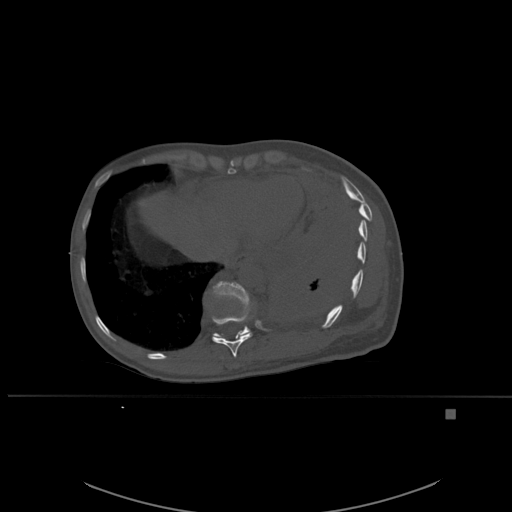
CT including the spine, one axial slice. Slice 312 of 537 in the series (ordered by position). Bone window (W 1800 / L 400 HU). 1.5 mm slice thickness. 512 × 512 image matrix. Female patient, age 45 years. Case-level facts recorded for this patient, not image findings: primary cancer: lung.
Annotated regions visible in this slice (semi-automatically segmented with operator editing):
- T10 vertebra: box from (x=212, y=298) to (x=253, y=358) px
- T11 vertebra: (x=212, y=281)–(x=252, y=338)